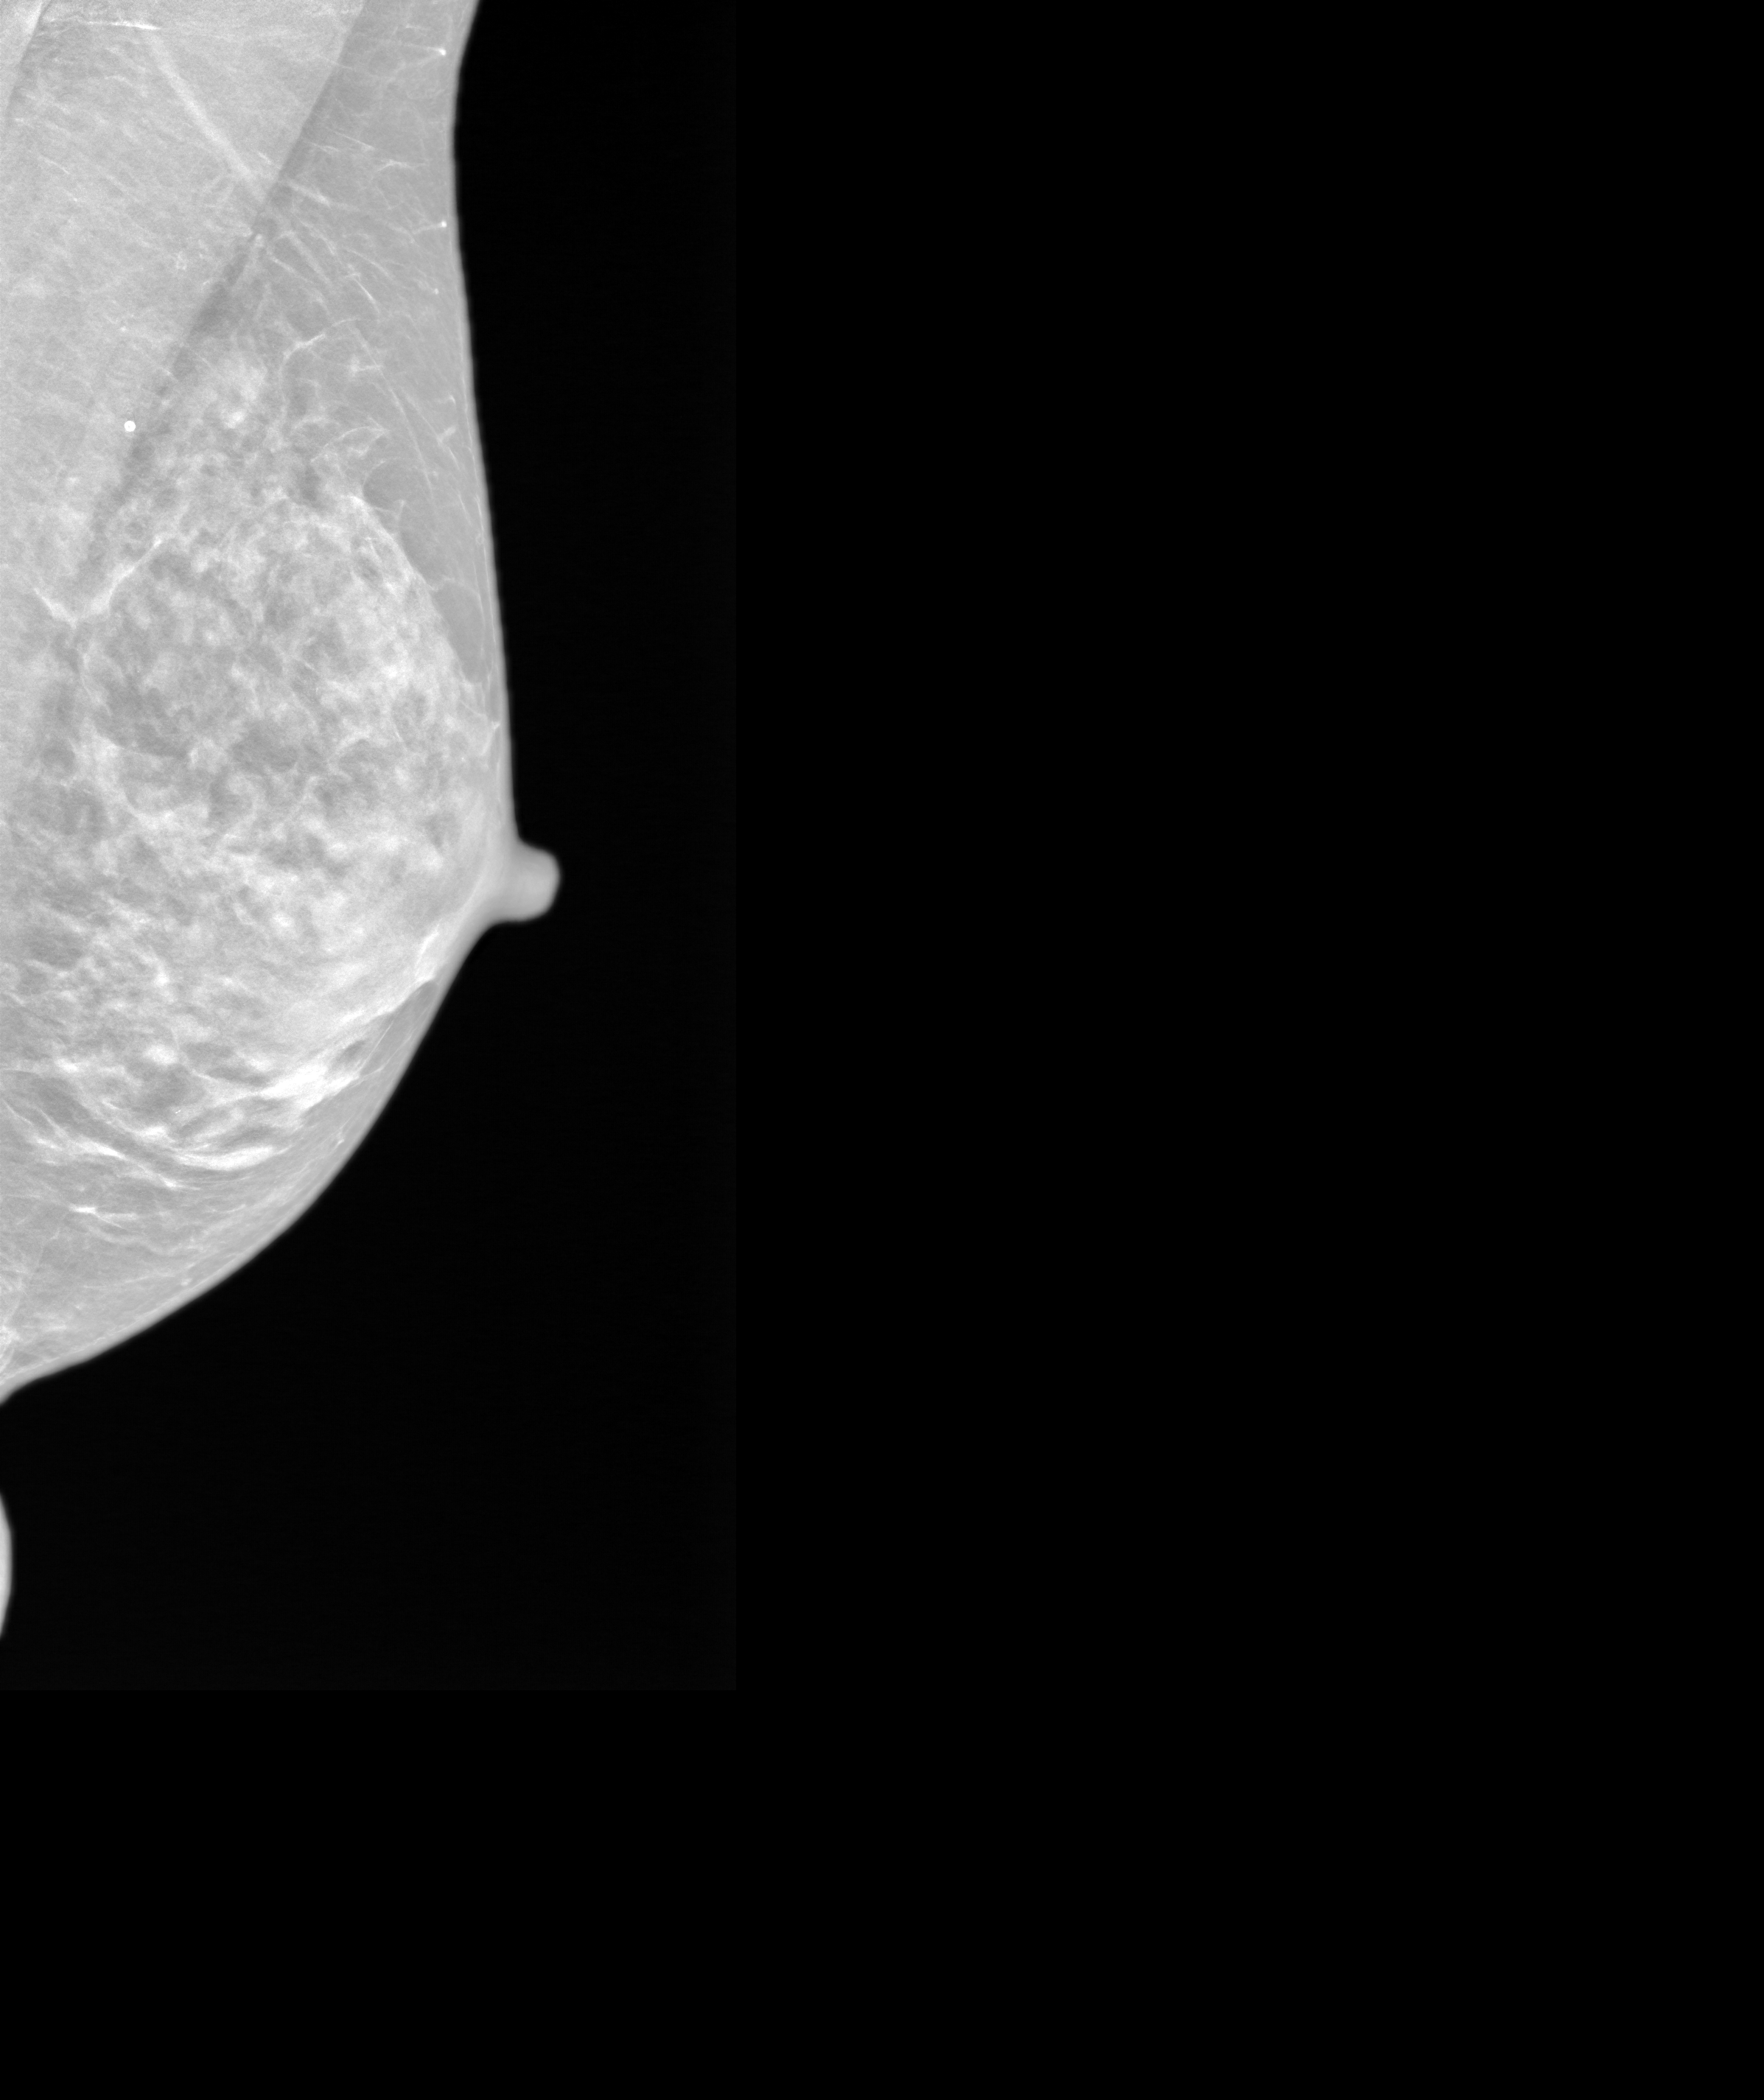
Screening examination; system: SenoIris_1SP2(440). Patient aged 68 years (female).
Image type: synthesized 2-D view from tomosynthesis. Breast: left. Projection: mediolateral oblique (MLO) view.